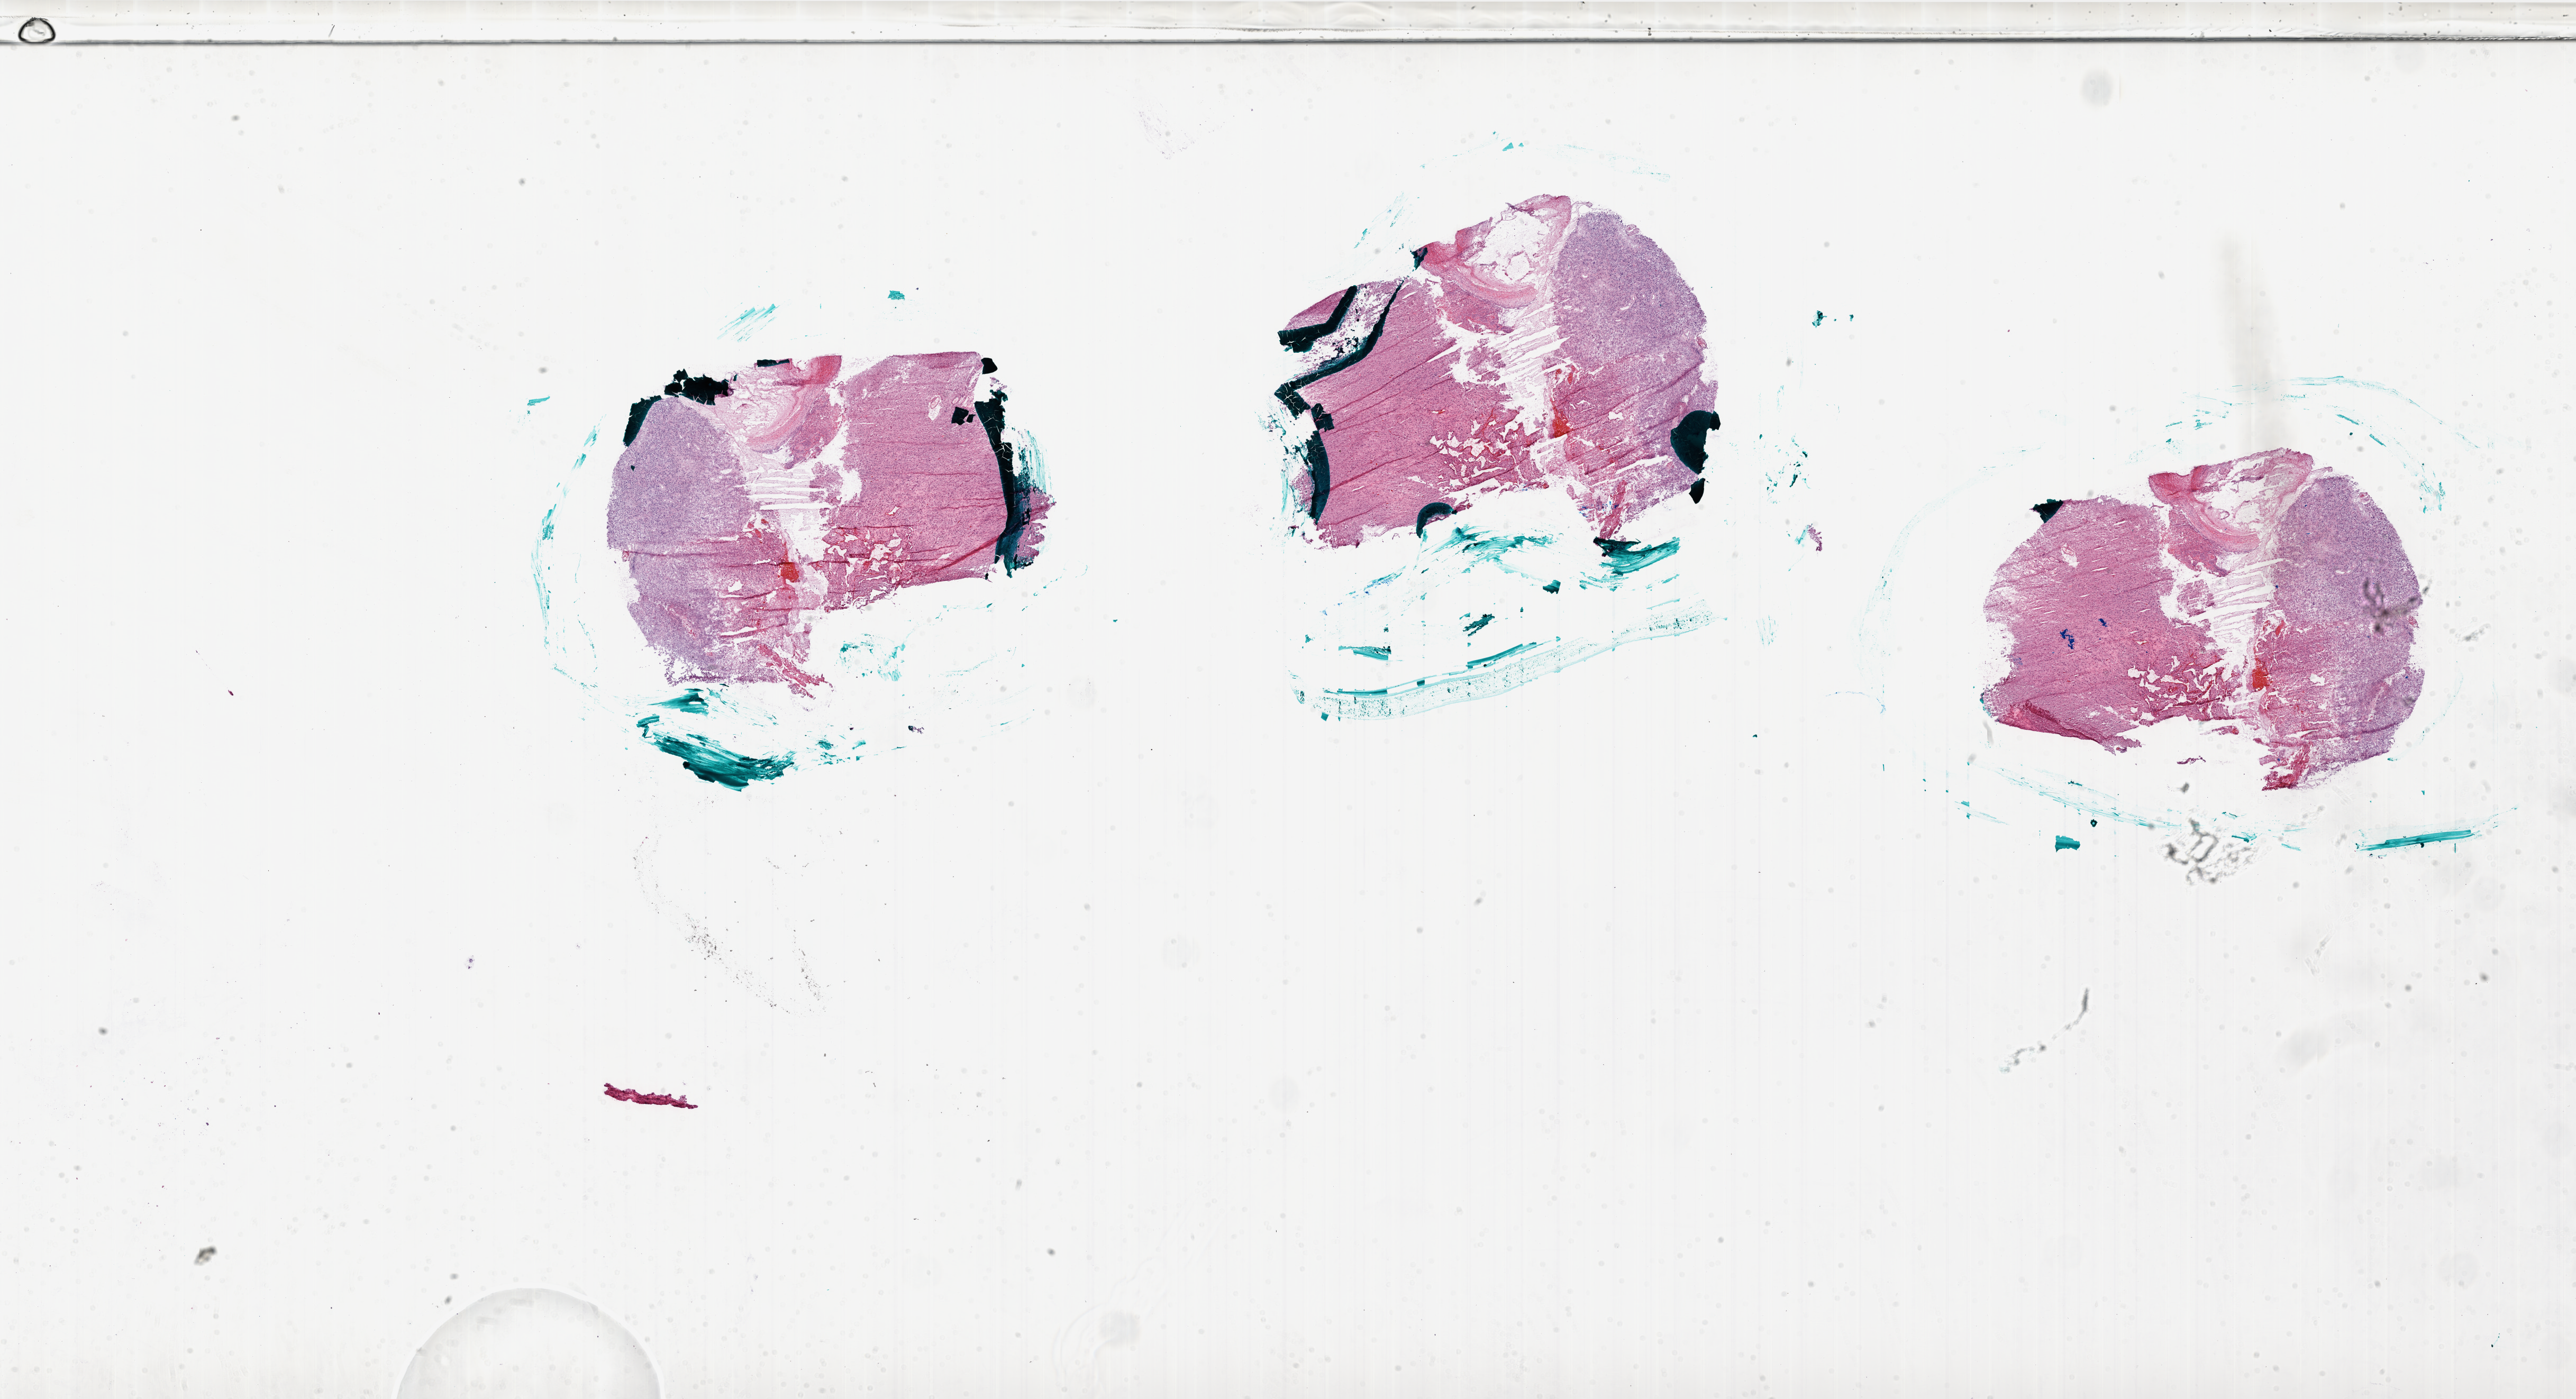
Digitized H&E-stained tissue section (whole slide), whole scanned area (about 39.0 x 21.2 mm, acquisition: 20x scan) shown as a low-resolution overview. Frozen section from the bottom of the tissue portion. Brain, primary tumour sample. Male patient; age at initial diagnosis 76 years. Pathologist review of this section (percent, as recorded): tumour cells 50%, tumour nuclei 90%, normal cells 0%, stromal cells 40%, necrosis 10%.
• pathologic diagnosis: Glioblastoma